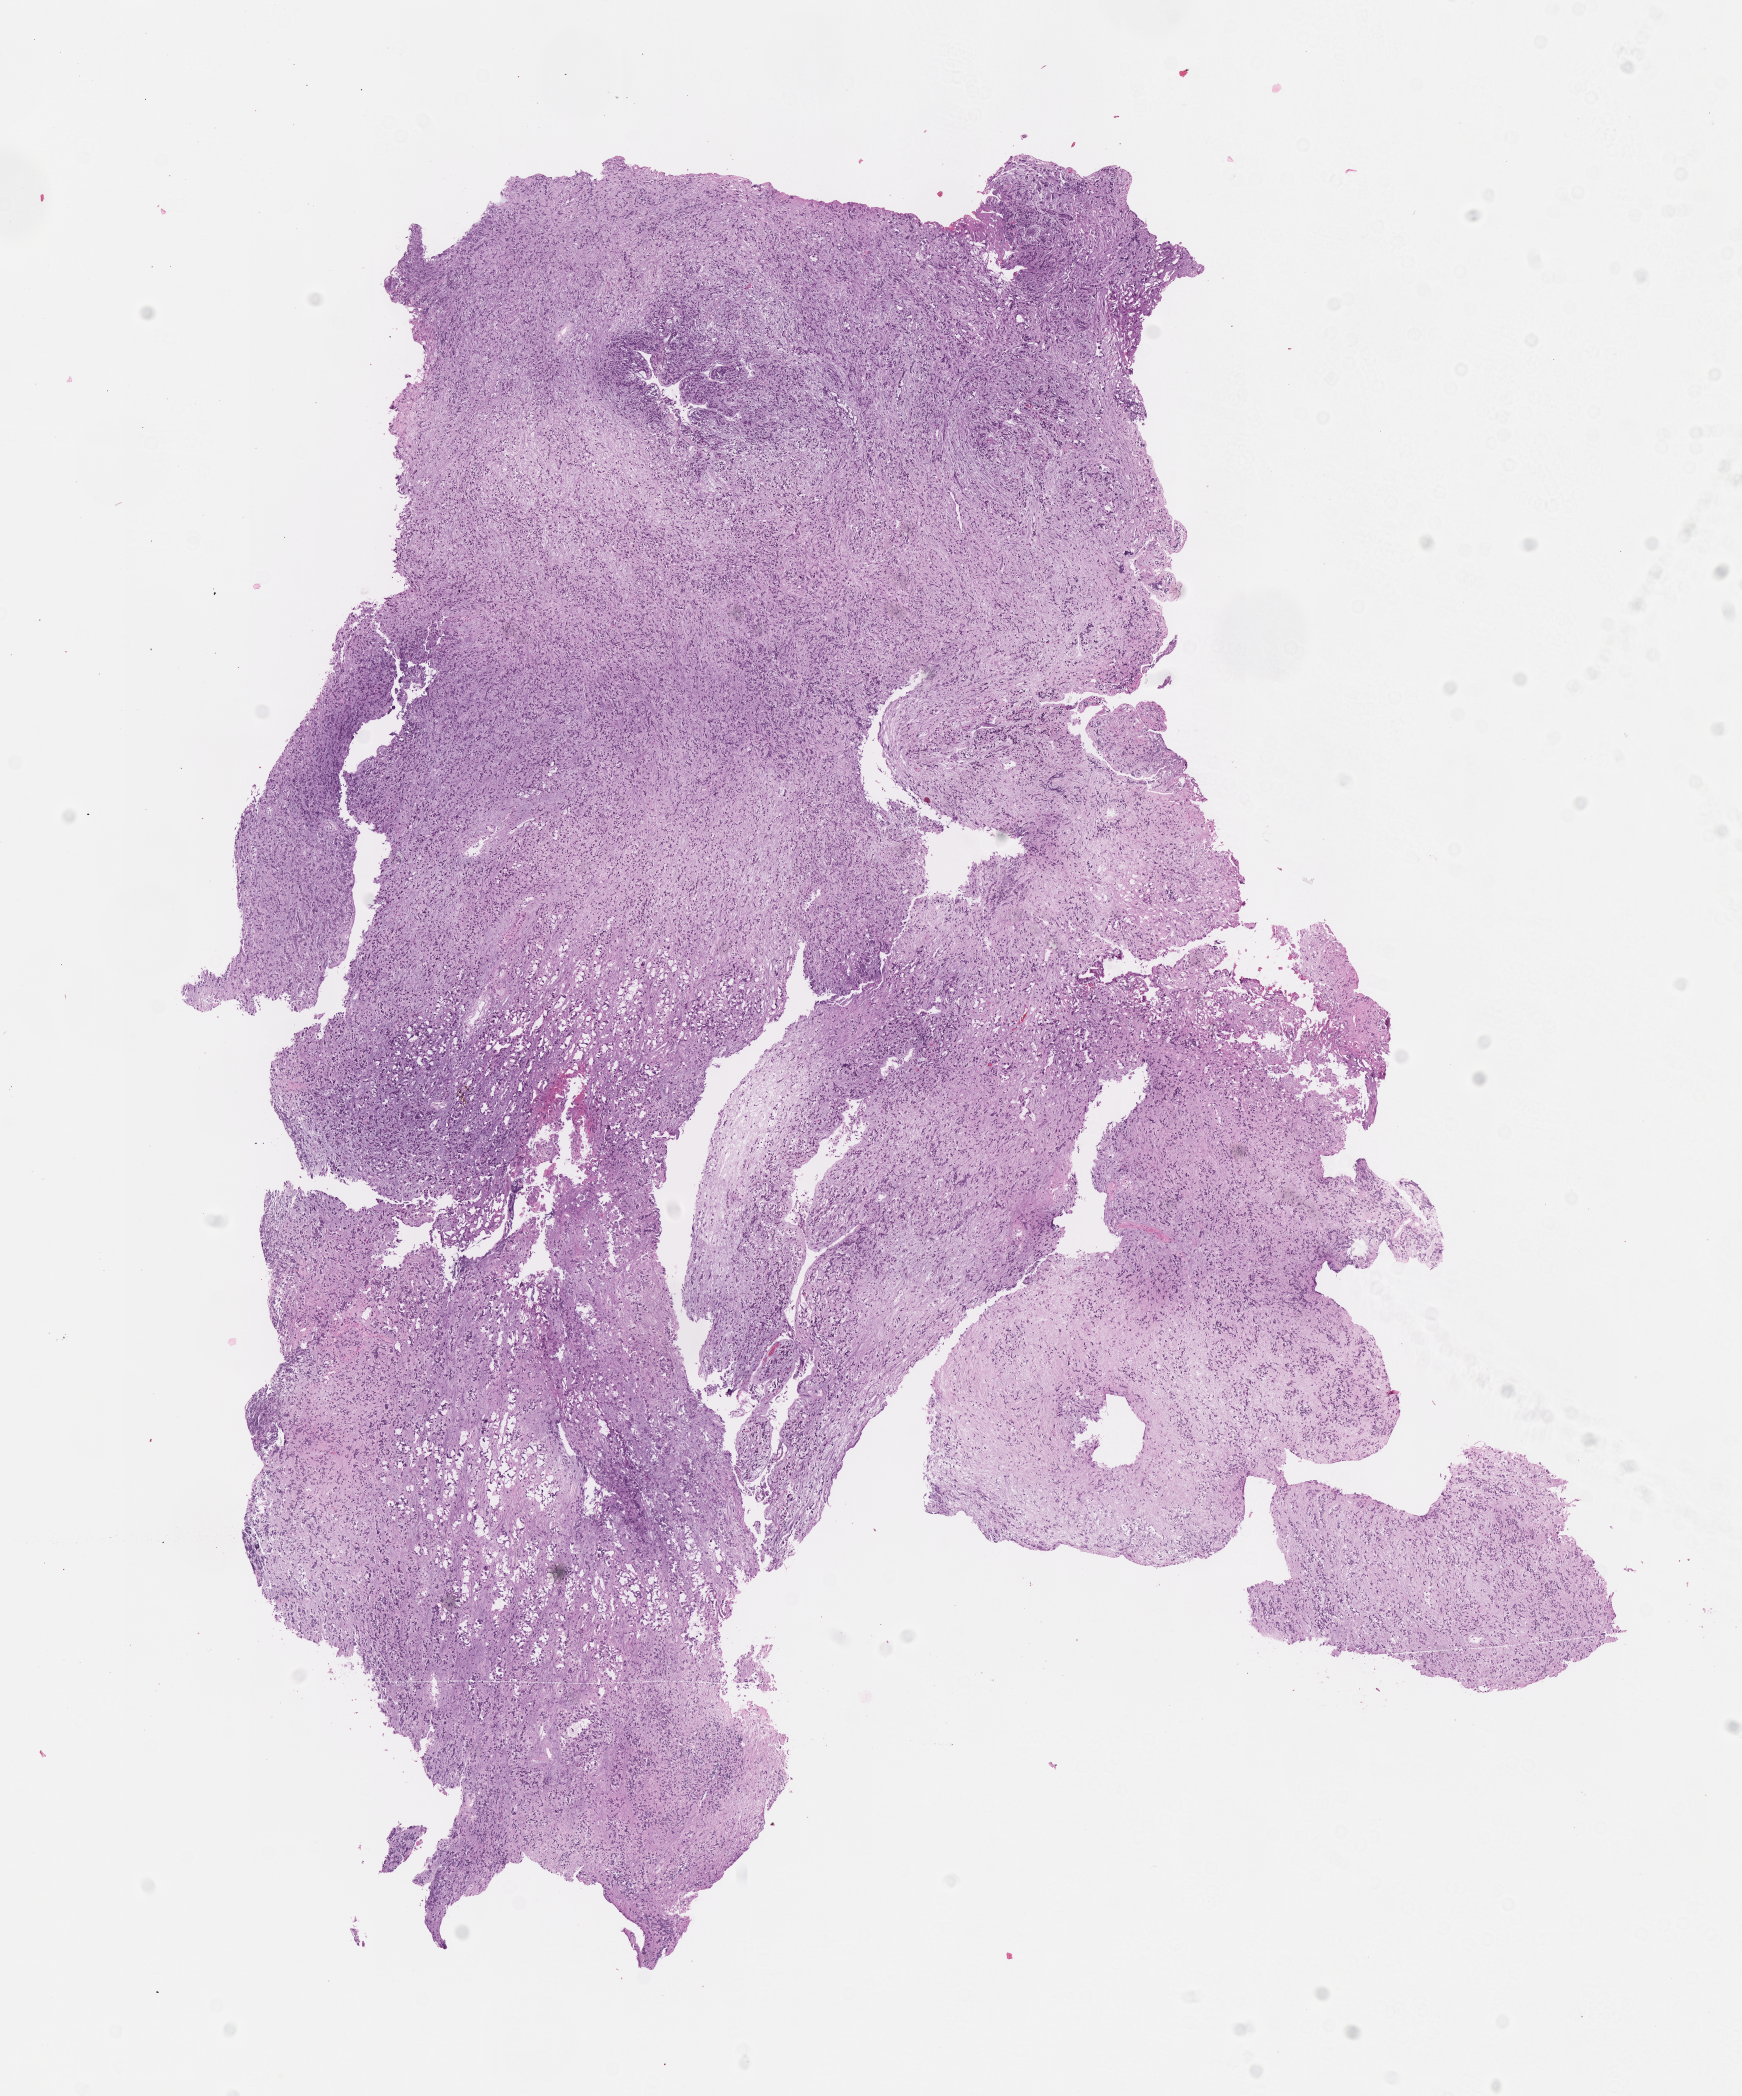
Digitized hematoxylin and eosin (H&E)-stained section of tumor tissue, a low-resolution overview of the entire scanned area, about 7.0 x 8.5 mm. Formalin-fixed paraffin-embedded section. Site: prostate. Male patient, age at diagnosis 12.8 years.
* metastatic status at presentation (as recorded): metastatic (confirmed)
* diagnosis: rhabdomyosarcoma; histological classification: embryonal rhabdomyosarcoma
* stage (as recorded): 4